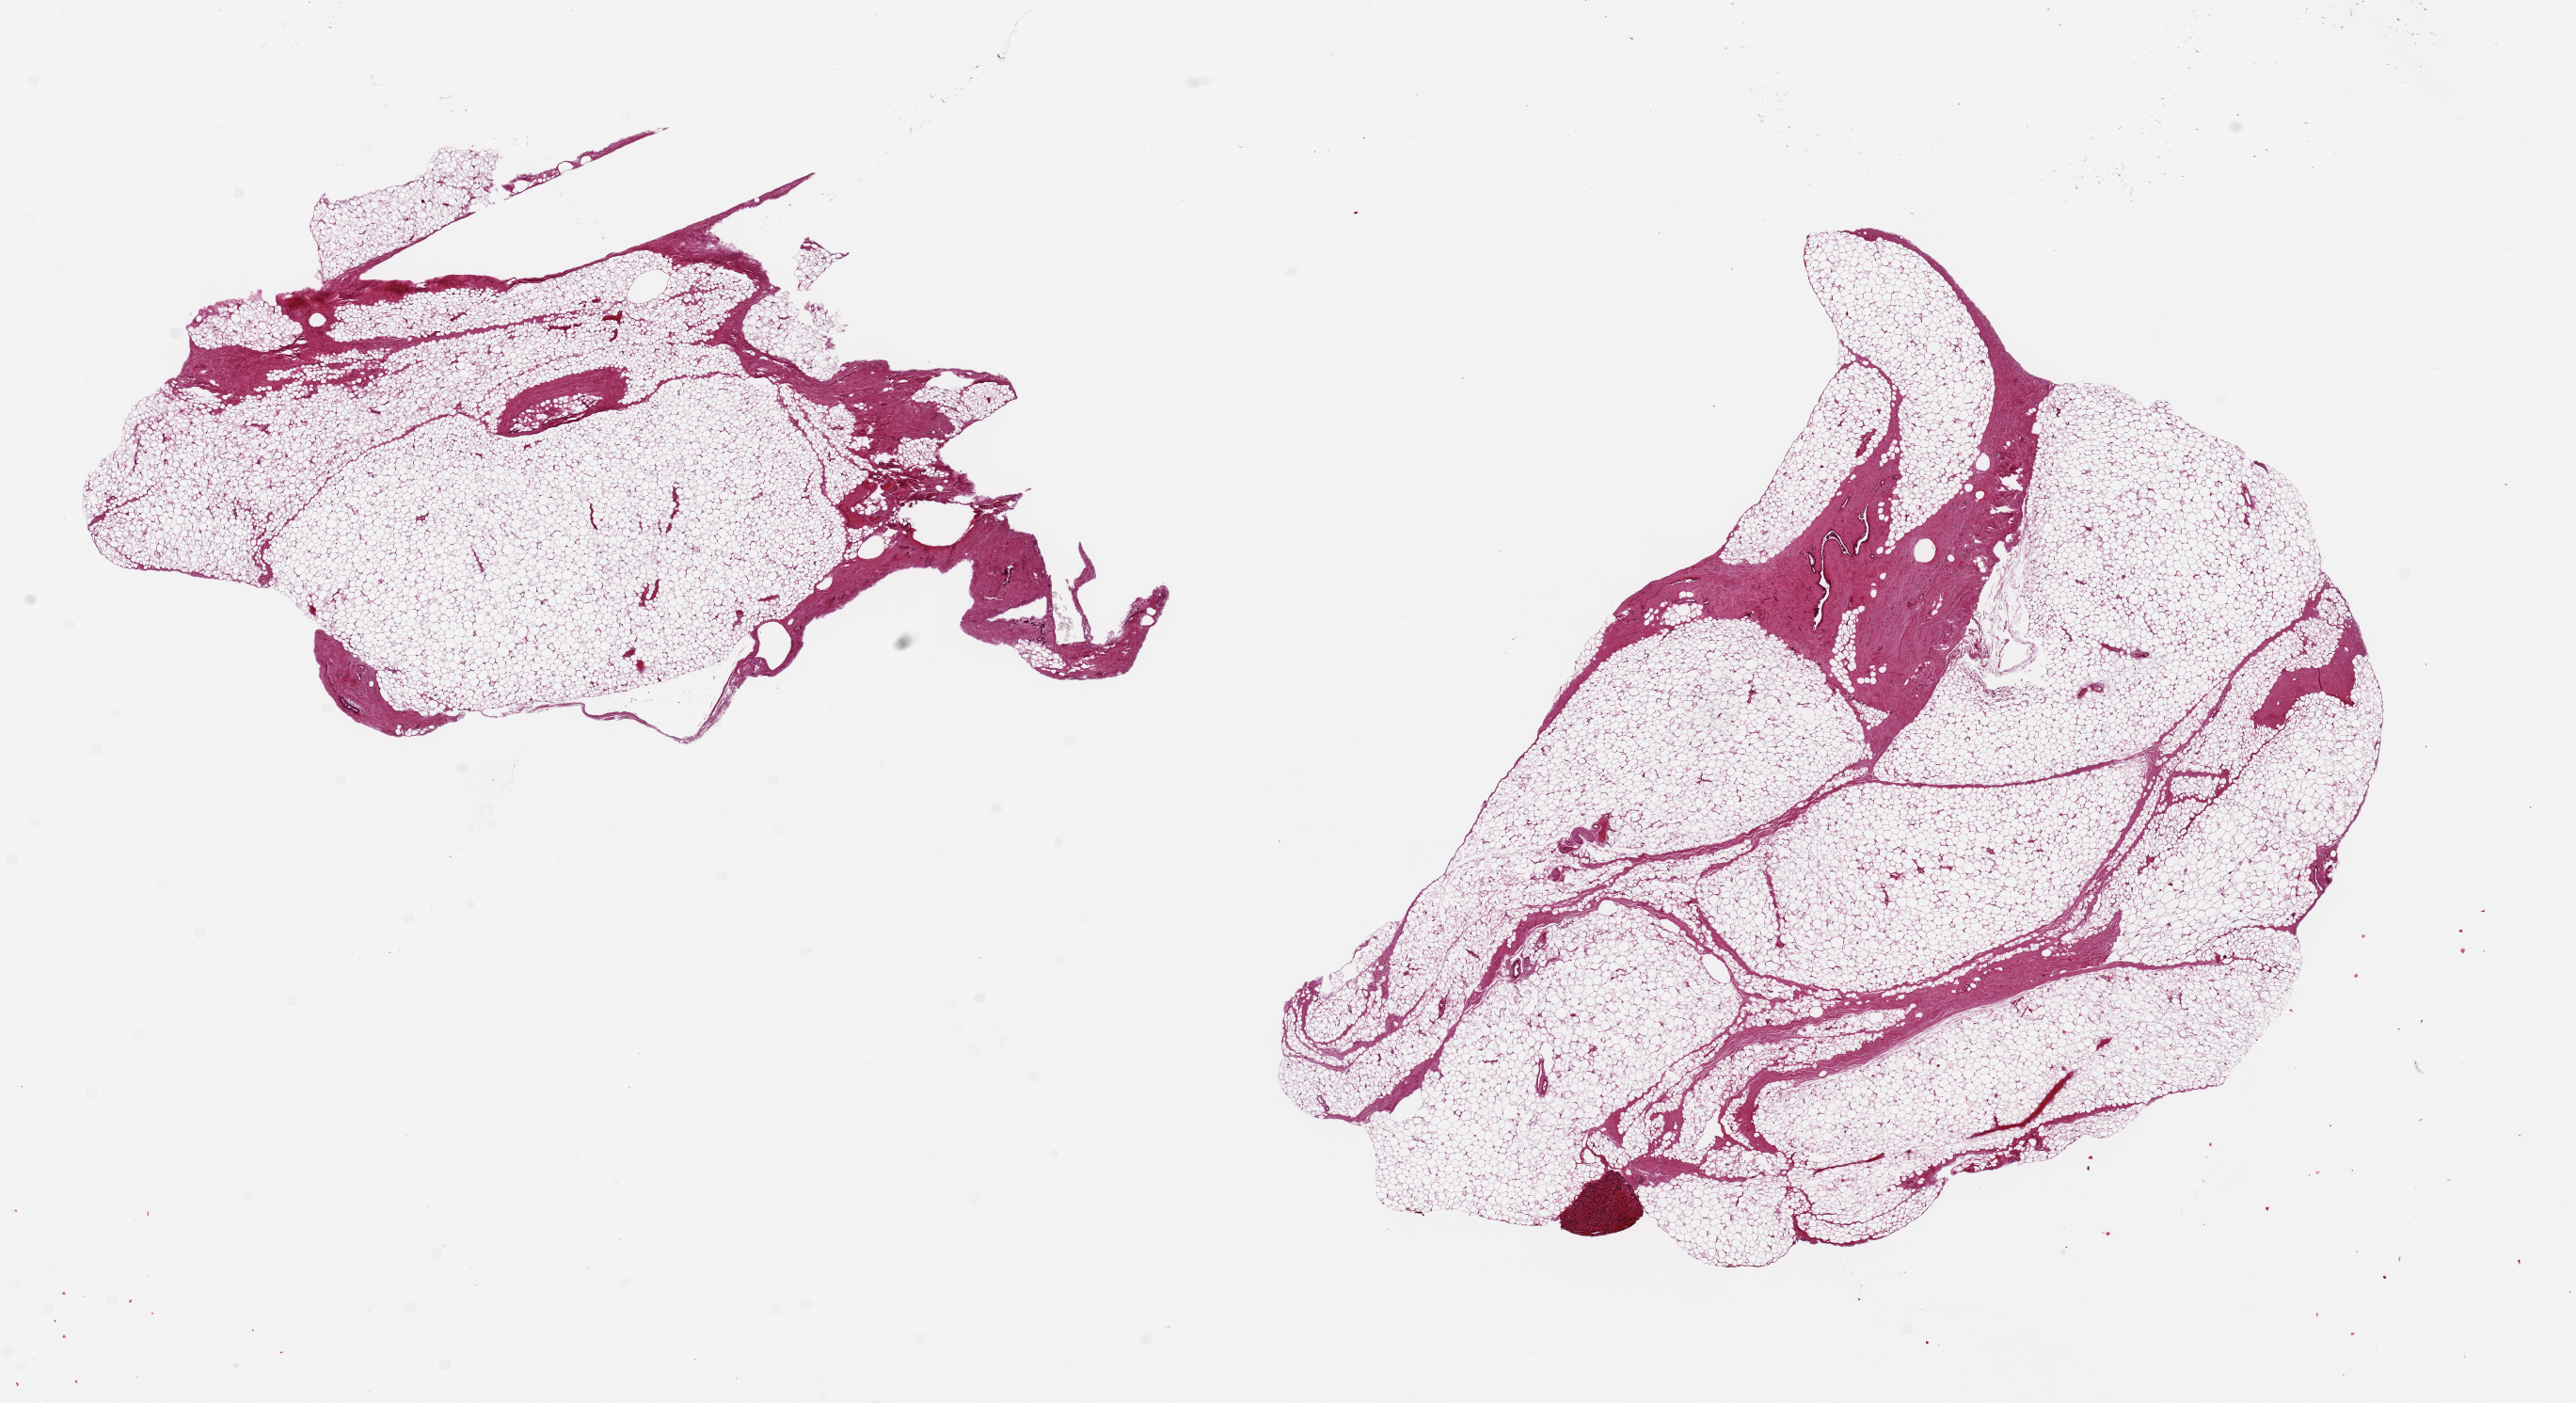
Whole-slide image, H&E stain — whole scanned area (about 21.7 x 11.8 mm, slide scanned at 20x) shown as a low-resolution overview. PAXgene-fixed paraffin-embedded (PFPE) section. Sampled site (target tissue): breast. Tissue donor sample. Donor: male.
Review note (as recorded): 2 pieces, one iwth trace focal ductal epithelium.